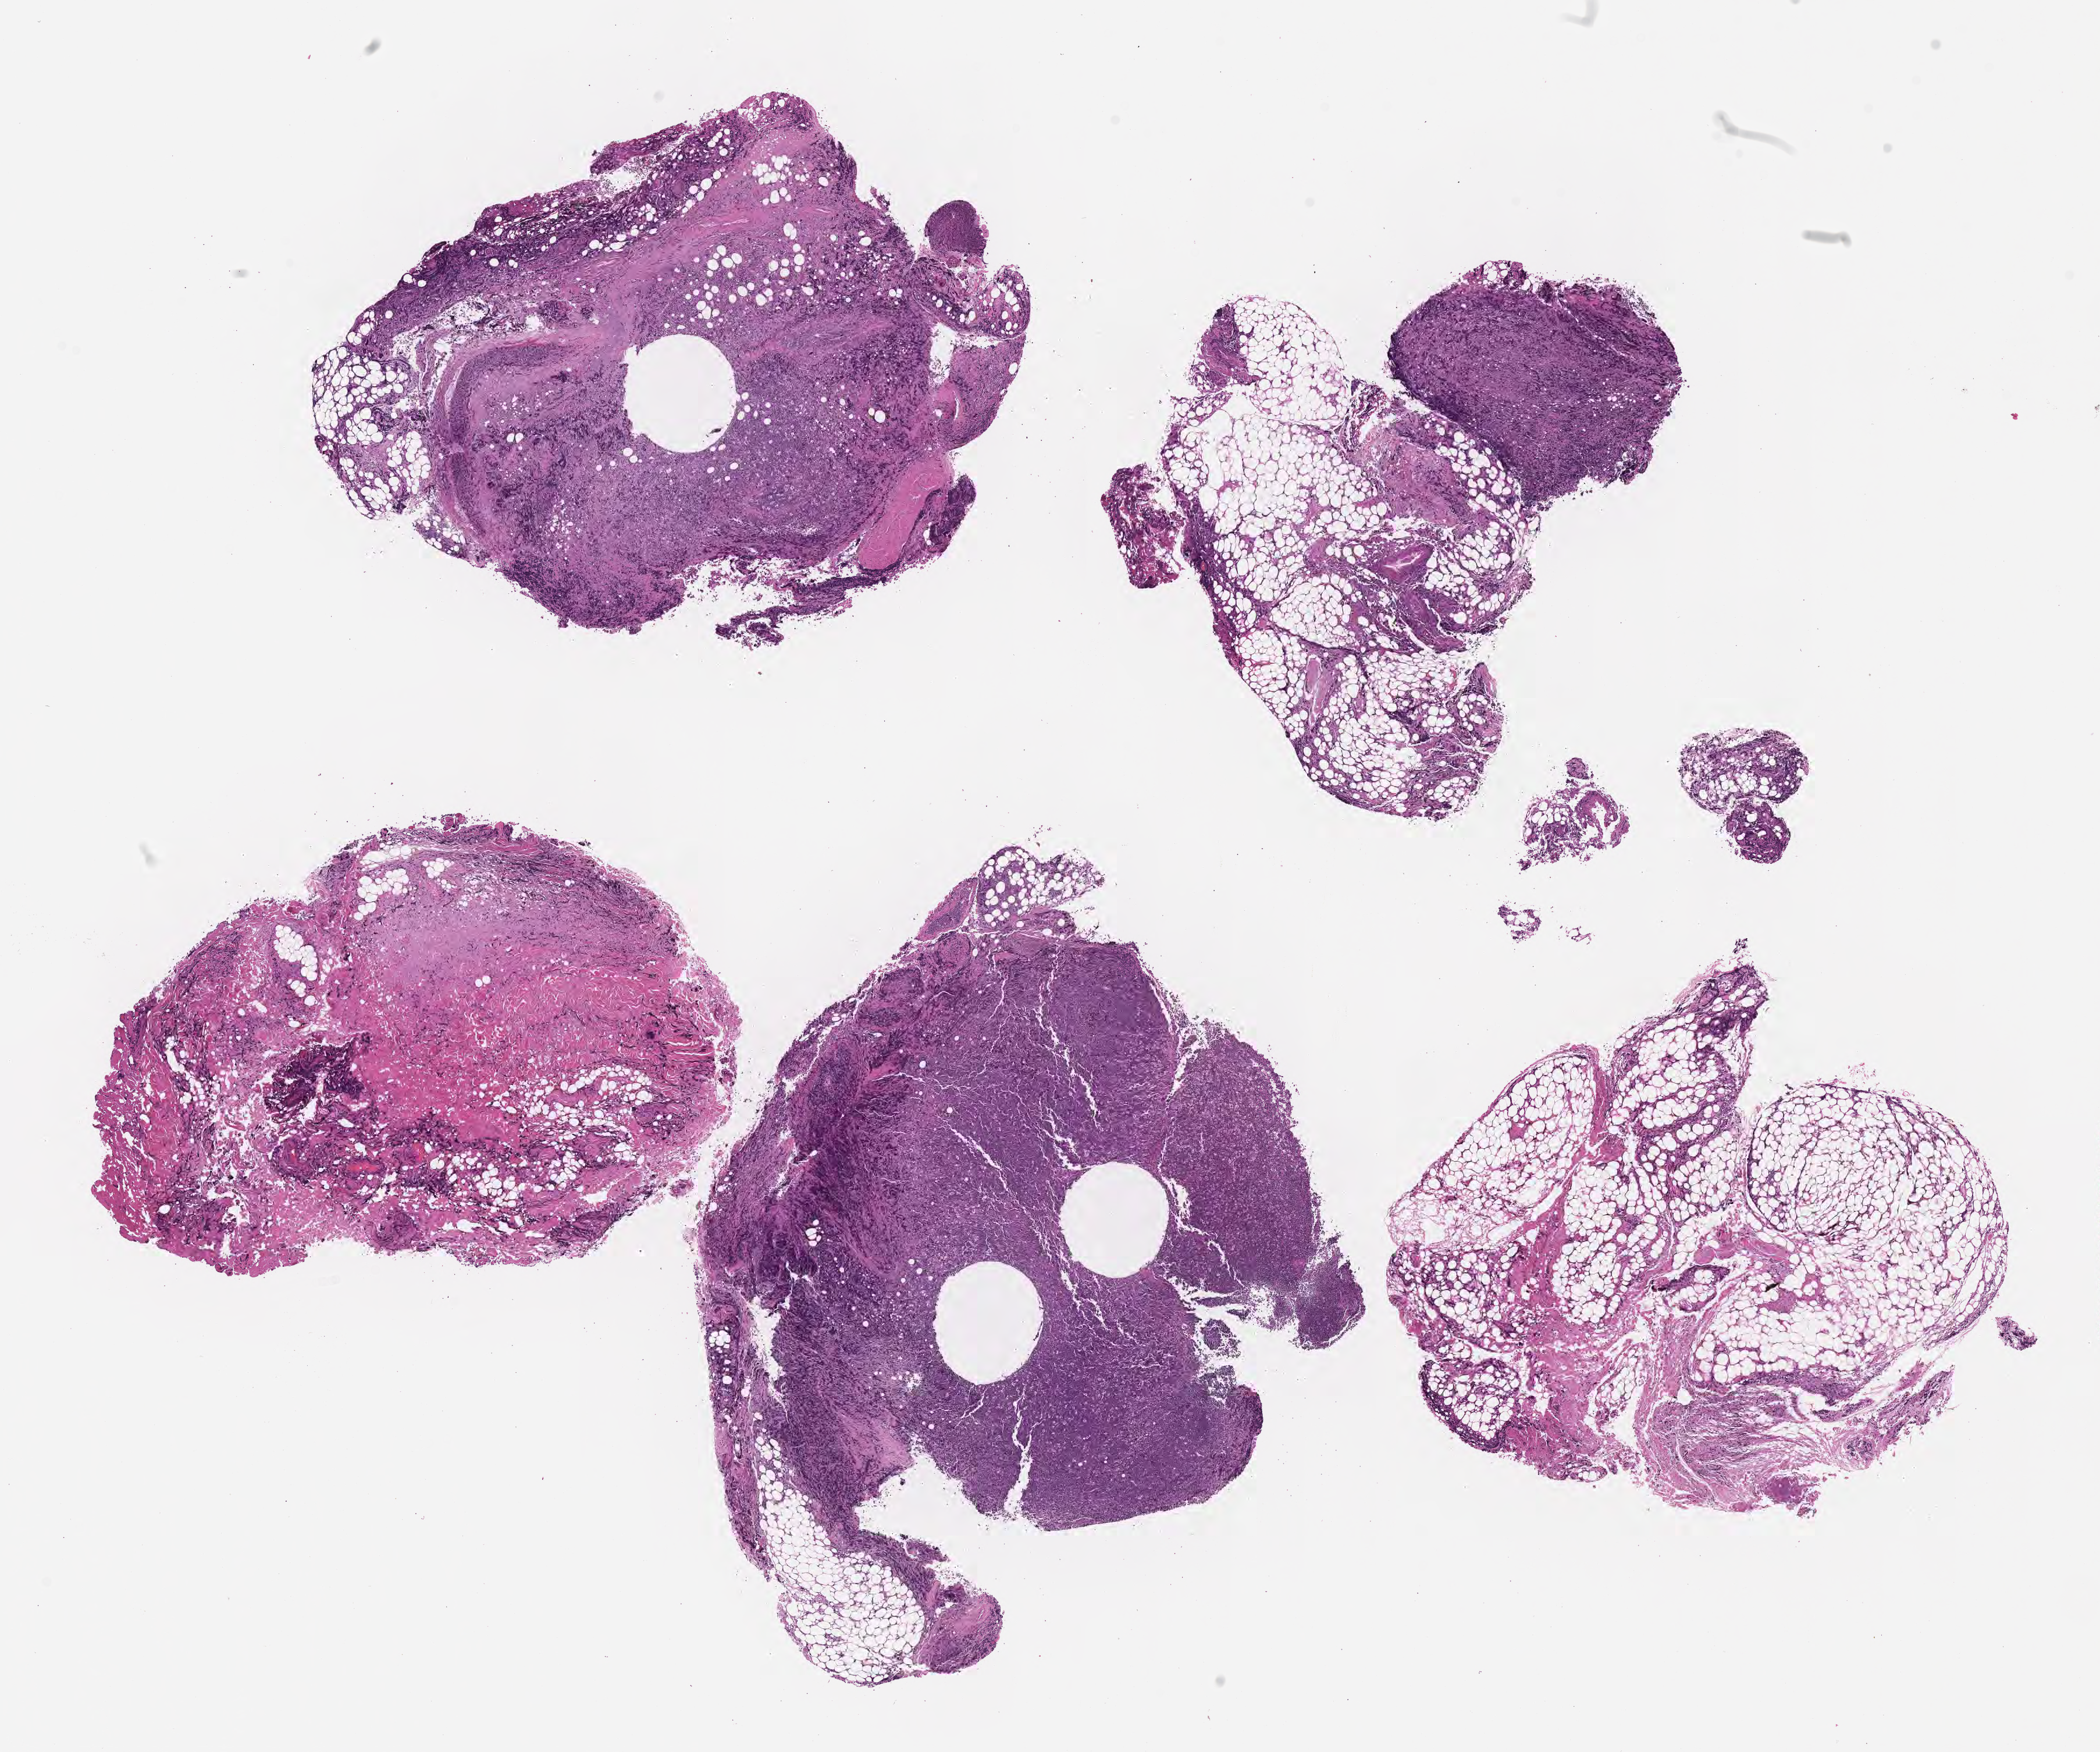
Whole-slide image, haematoxylin and eosin stain — low-resolution overview of the scanned area, about 14.6 x 12.2 mm, formalin-fixed paraffin-embedded section, primary tumor. Patient: male, age 54 years. Slide review estimates, as recorded: tumor cells 60%, tumor nuclei 85%, stromal cells 5%, necrosis 5%, normal cells 30%. Infiltration values recorded for this section: lymphocyte infiltration 50%, monocyte infiltration 20%, neutrophil infiltration 5%.
Section: top of the tissue portion. Histologic diagnosis: Burkitt lymphoma, NOS. Ann Arbor stage (patient): Stage IV.